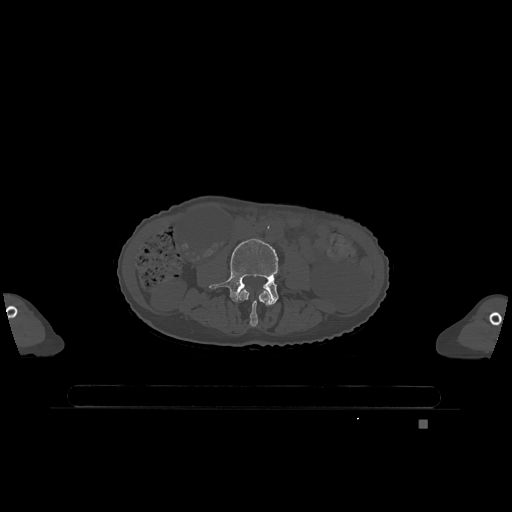
CT including the spine, one axial slice. Slice 318 of 1317 in the series (ordered by position). Bone window (W 1800 / L 400 HU). 0.5 mm slice thickness. 512 × 512 image matrix, field of view 500 × 500 mm. Female patient, age 74 years. Case-level facts recorded for this patient, not image findings: primary cancer: lung; vertebrae with lytic lesions (as recorded): T1, T4, T5, T6, L4, L5.
Structures marked on this image (semi-automatic segmentation, software-assisted and operator-edited):
- L3 vertebra: bounding box [x1, y1, x2, y2] px = [239, 289, 270, 327]
- L4 vertebra: [209, 239, 279, 305]